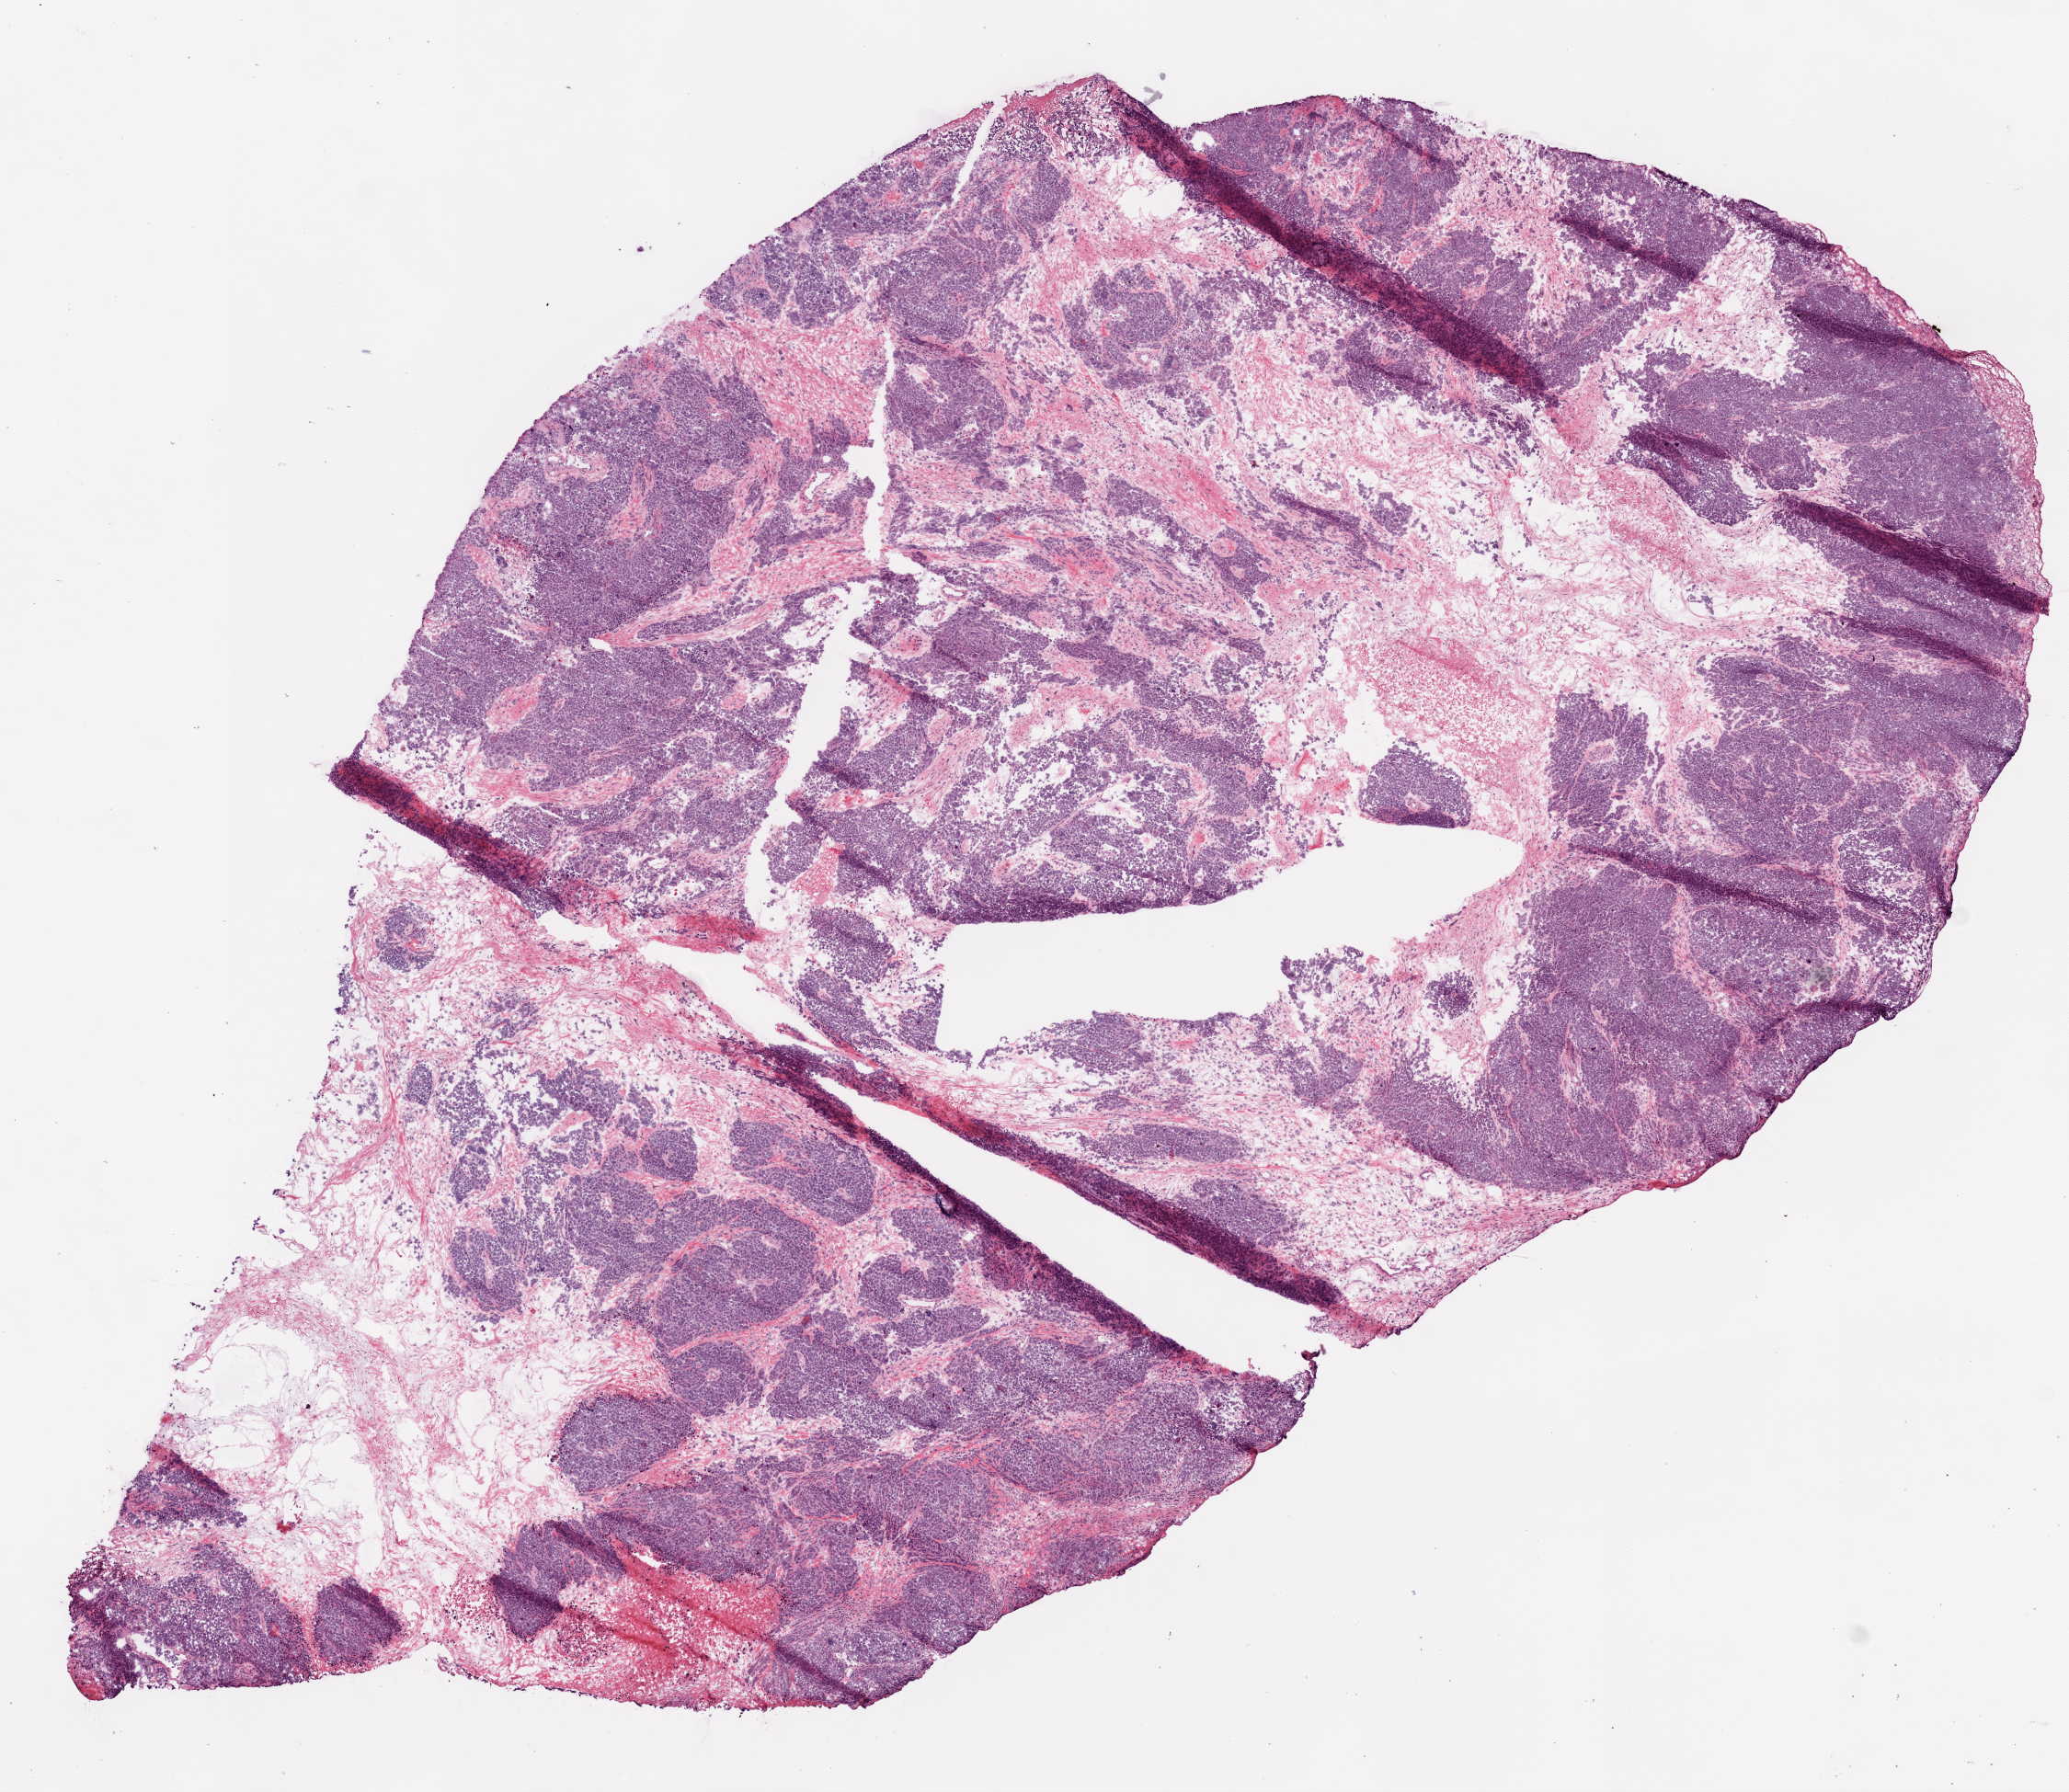
Digitized Hematoxylin and eosin (H&E) stained tissue section (whole slide) — low-resolution overview of the scanned area, about 9.0 x 7.8 mm. Frozen section. Ovary, primary tumour sample. Patient: female, age at initial diagnosis 65 years. Histologic grade: G3 (poorly differentiated). Composition of this section per pathologist review: tumour cells 65%, tumour nuclei 95%, normal cells 0%, stromal cells 30%, necrosis 5%. Inflammatory infiltration, as recorded: lymphocyte infiltration 2%.
Laterality: right. FIGO stage: IIIC. Diagnosis: Serous cystadenocarcinoma, NOS.